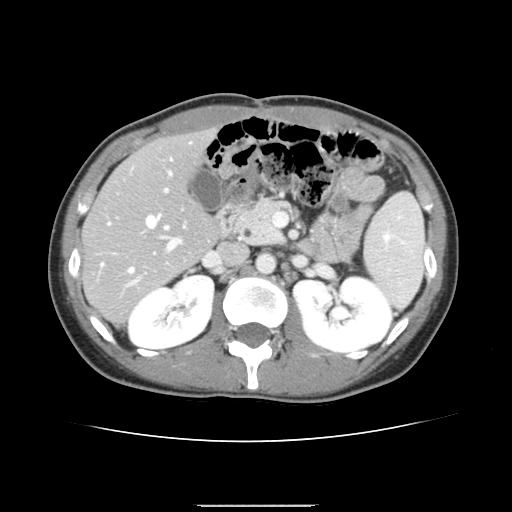
Contrast-enhanced abdominal CT, one axial slice. Position 80 of 150 along the scan axis. Intravenous contrast given. Soft-tissue window (W 400 / L 40 HU). 2.5 mm slice thickness. 512 × 512 image matrix. Female patient, age 32 years. From the clinical record (not read from this slice): diagnosis: colorectal cancer liver metastases, imaged before liver resection.
Structures marked on this image (expert manual segmentation):
- hepatic veins: bounding box <101,215,168,272> (left, top, right, bottom; pixels)
- liver: <84,131,218,322>
- planned liver remnant (the part of the liver to remain after resection): <84,131,218,277>
- portal vein (with intrahepatic branches): <128,171,185,285>